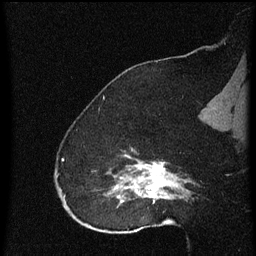
Breast MRI (dynamic contrast-enhanced), one sagittal slice; position 43 of 60 along the scan axis; dynamic contrast-enhanced series, image 2 of 4 at this slice position (ordered by acquisition); 1.5 T; TE 4.2 ms, TR 8 ms; 2 mm slice thickness; 256 × 256 image matrix. Patient: female, 52 years.
Annotated regions visible in this slice (semi-automatic segmentation, software-assisted and operator-edited):
- analysis volume of interest (the breast-tissue region the enhancement analysis was run in; not a lesion): bounding box [x1, y1, x2, y2] px = [73, 148, 172, 219]
- tumour enhancement mask (voxels above the 70 % enhancement threshold inside the analysis volume of interest): [116, 156, 172, 205]